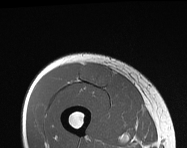
MRI of an extremity soft-tissue mass, one axial slice. Slice 46 of 114 in the series (ordered by position). MR volume resampled by the dataset authors to the PET/CT grid (not the native acquisition matrix). 3.27 mm slice thickness. 187 × 148 image matrix, field of view 183 × 145 mm. Male patient. From the clinical record (not read from this slice): histological type: pleiomorphic leiomyosarcoma; grade: intermediate; site of the primary tumour: right thigh.
Outlined on this slice (expert contour drawn on MRI and transferred to this co-registered scan by the dataset authors):
- gross tumour volume including surrounding oedema: box from (x=80, y=63) to (x=113, y=87) px